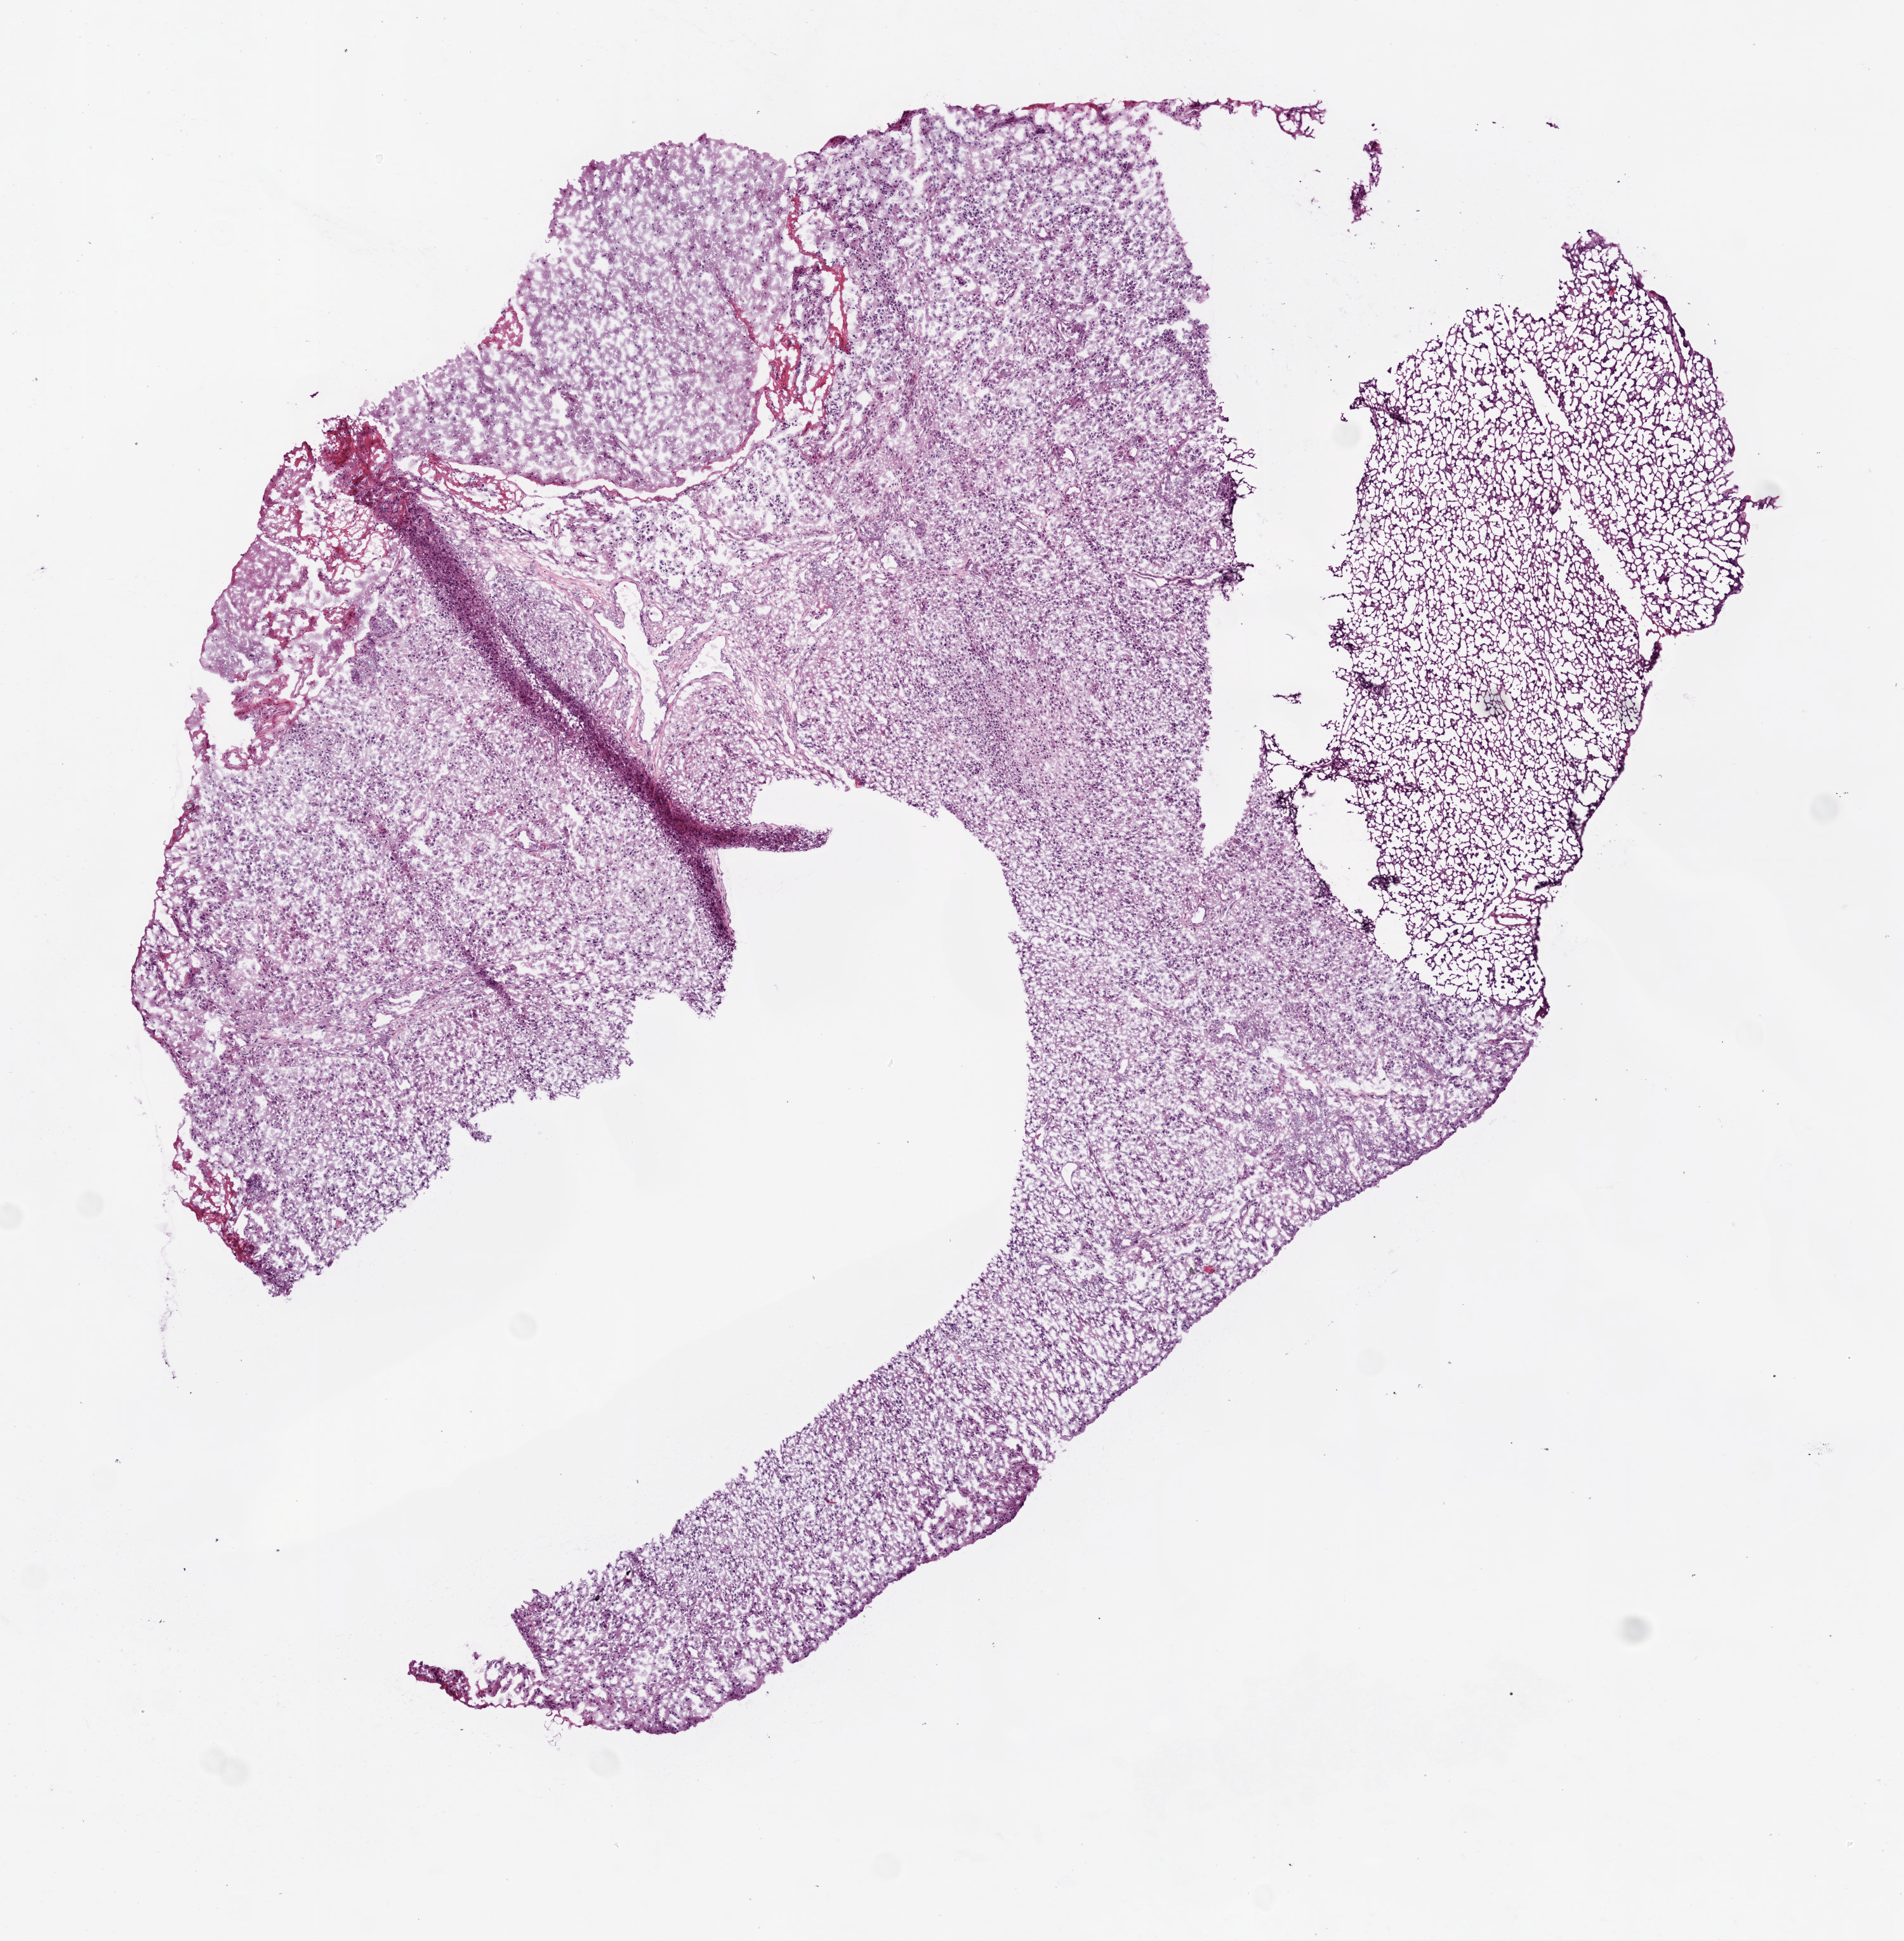
Digitized H&E-stained tissue section (whole slide), low-resolution overview of the scanned area, about 6.0 x 6.1 mm, frozen section from the bottom of the tissue portion, primary tumour sample from the brain. Patient: male, age at initial diagnosis 73 years. Composition of this section per pathologist review: tumour cells 70%, tumour nuclei 80%, normal cells 20%, stromal cells 10%, necrosis 0%. Infiltration values recorded for this section: lymphocyte infiltration 100%.
- diagnosis: Glioblastoma